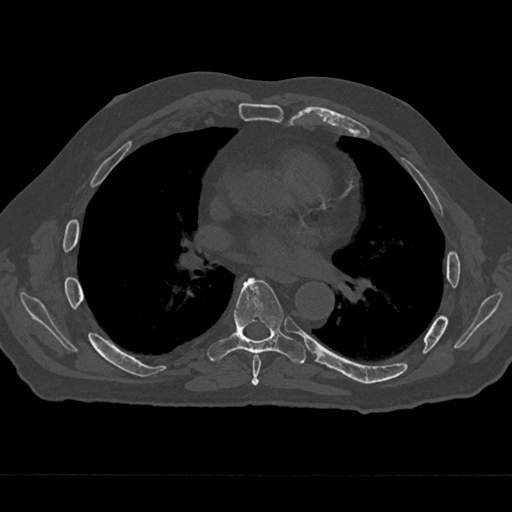
CT including the spine, one axial slice. Position 379 of 797 along the scan axis. 120 kVp. Bone window (W 1800 / L 400 HU). 0.5 mm slice thickness. 512 × 512 image matrix, field of view 377 × 377 mm. Male patient, age 75 years. Case-level facts recorded for this patient, not image findings: primary cancer: renal; vertebrae with lytic lesions (as recorded): T4.
Annotated regions visible in this slice (semi-automatically segmented with operator editing):
- T6 vertebra: bounding box (x1, y1, x2, y2) in pixels: (252, 354, 261, 386)
- T7 vertebra: (207, 278, 306, 364)